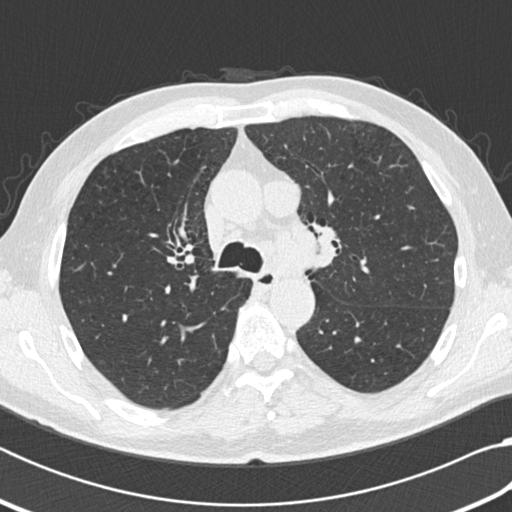
Low-dose screening chest CT, axial slice; third annual screen; lung window (W 1500 / L -600 HU); 2 mm slice thickness; standard (soft-tissue) reconstruction kernel (B30f); 120 kVp; slice 68 of 207 in the series. Male participant, aged 64 years at enrolment. Current smoker at enrolment.
• Expert reader's lesion annotation, box from (x=252, y=176) to (x=295, y=216) px.
• No non-calcified nodule or mass ≥4 mm was recorded by the screening reader at this exam.
• Official screen result: negative screen, significant abnormalities not suspicious for lung cancer.
• Later outcome: lung cancer diagnosed 163 days after this screen — small cell carcinoma, NOS, mediastinum, stage IV (AJCC 6th edition).